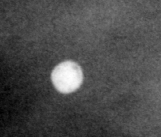
Crop from a digitized film mammogram around one marked abnormality; left breast; CC view; BI-RADS breast density category 4 (scale 1–4).
Calcifications, morphology round and regular / lucent center / punctate, distribution diffusely scattered; BI-RADS assessment category 2; subtlety rating 5 on a 1 (subtle) to 5 (obvious) scale; benign without callback (not worked up further).